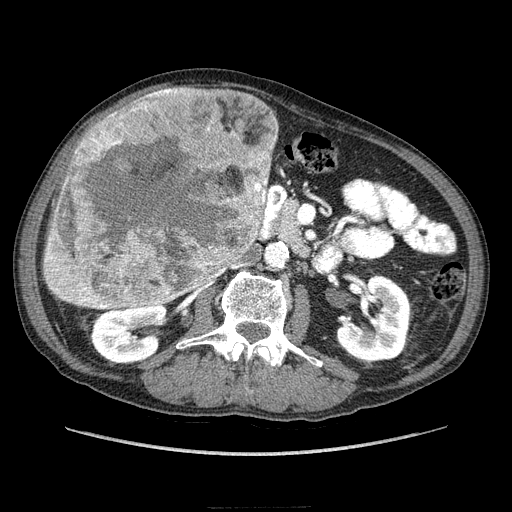
Contrast-enhanced abdominal CT (liver protocol), one axial slice. Slice 93 of 218 in the series (ordered by position). Soft-tissue window (W 400 / L 40 HU). 2.5 mm slice thickness. 512 × 512 image matrix, field of view 380 × 380 mm. Case-level facts recorded for this patient, not image findings: diagnosis: hepatocellular carcinoma (patient treated with transarterial chemoembolisation; whether this scan precedes or follows treatment is not stated here); TNM stage (as recorded): Stage-IIIA.
Annotated regions visible in this slice (semi-automatic segmentation, software-assisted and operator-edited):
- liver parenchyma outside the tumour (the mass and vessels are separate outlines, so this box may not span the whole liver): bounding box (x1, y1, x2, y2) in pixels: (103, 102, 278, 267)
- mass: (40, 87, 276, 312)